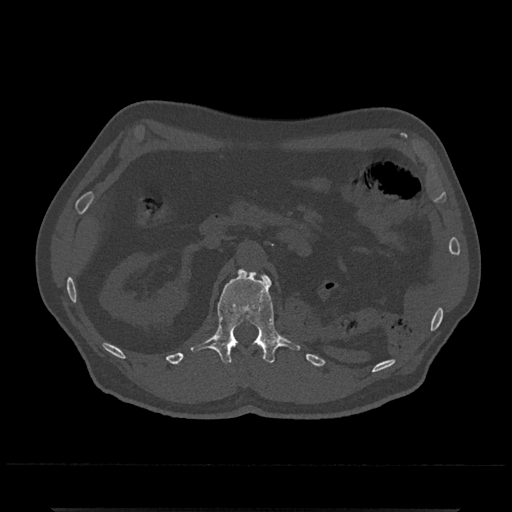
CT including the spine, one axial slice. Slice 370 of 797 in the series (ordered by position). Bone window (W 1800 / L 400 HU). 512 × 512 image matrix, field of view 393 × 393 mm. Patient: male, 67 years. From the clinical record (not read from this slice): primary cancer: prostate.
Annotated regions visible in this slice (semi-automatic segmentation, software-assisted and operator-edited):
- L1 vertebra: bounding box (x1, y1, x2, y2) in pixels: (190, 269, 301, 364)
- T12 vertebra: (259, 345, 264, 355)